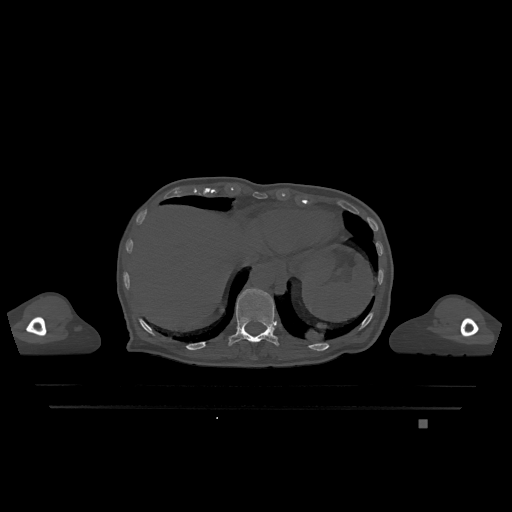
CT including the spine, one axial slice. Slice 591 of 1317 in the series (ordered by position). Bone window (W 1800 / L 400 HU). 0.5 mm slice thickness. 512 × 512 image matrix, field of view 500 × 500 mm. Patient: female, 74 years. Case-level facts recorded for this patient, not image findings: primary cancer: lung; vertebrae with lytic lesions (as recorded): T1, T4, T5, T6, L4, L5.
Annotated regions visible in this slice (semi-automatic segmentation, software-assisted and operator-edited):
- T11 vertebra: bounding box <228,289,279,346> (left, top, right, bottom; pixels)